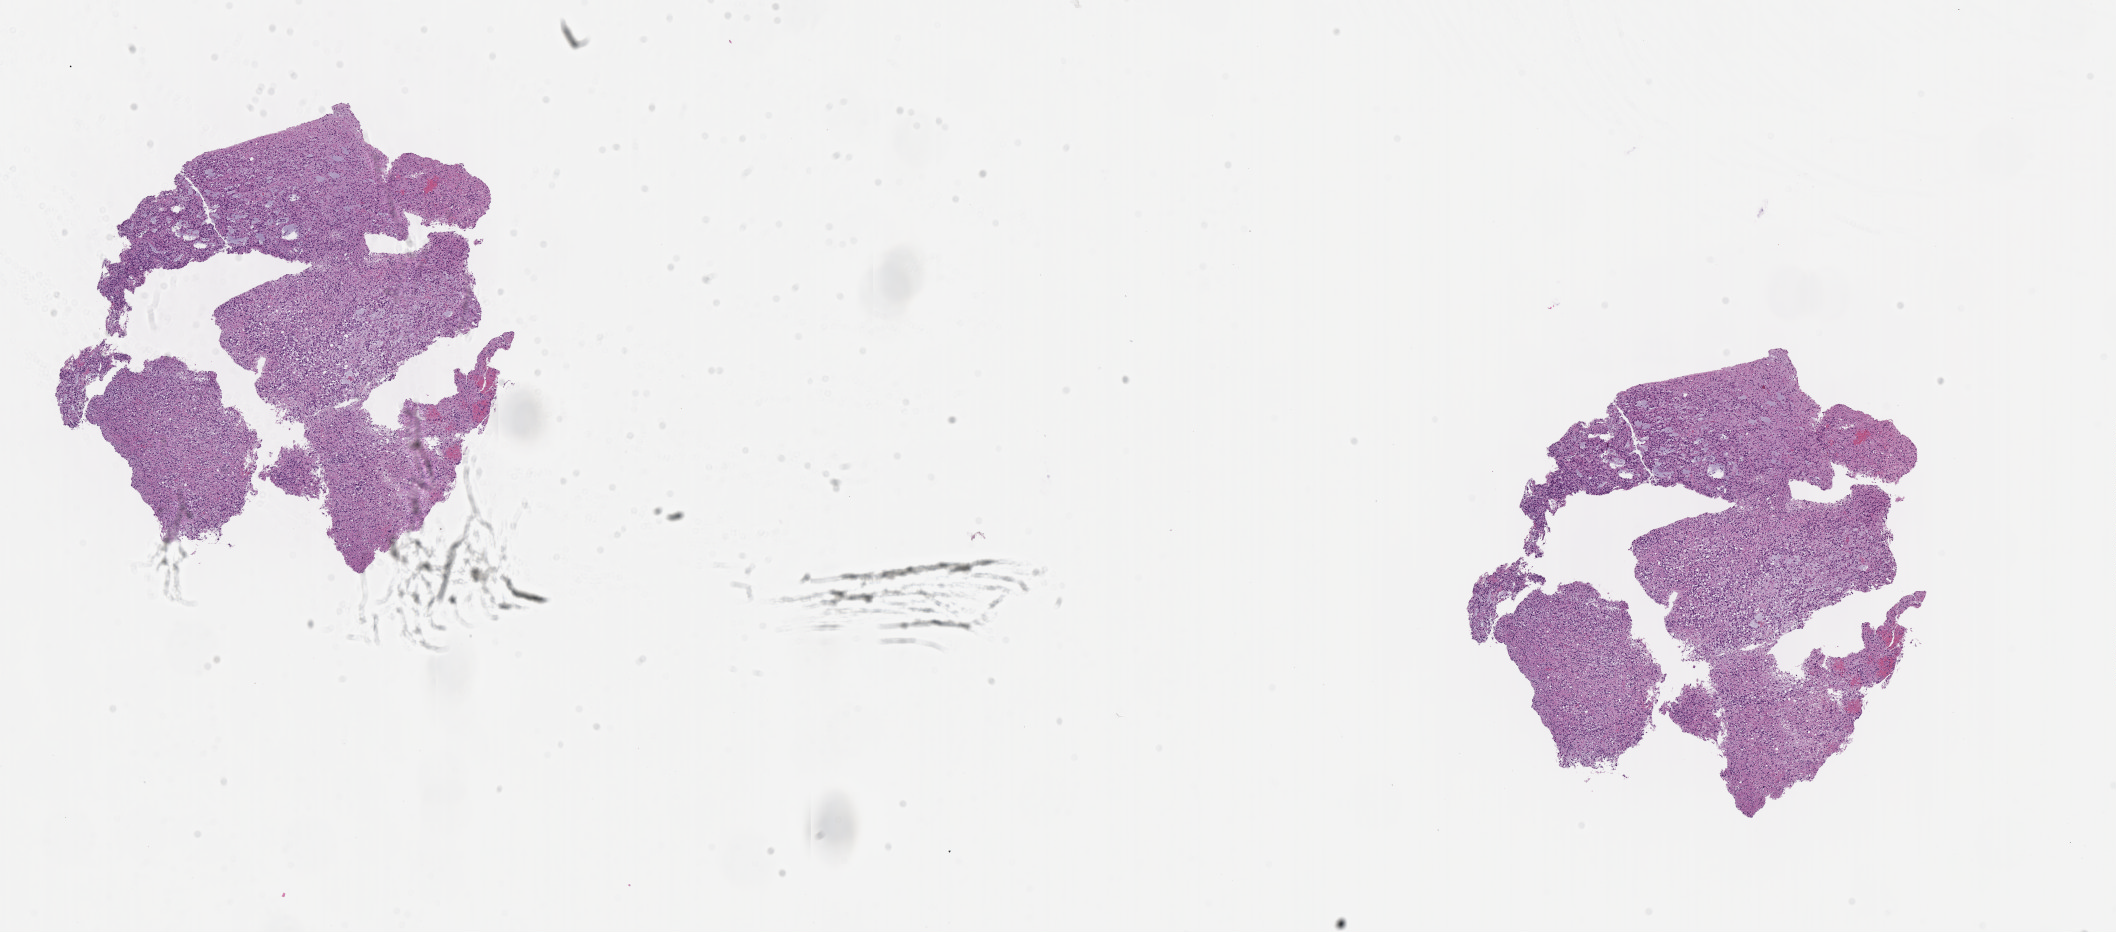
Digitized H&E tissue section (whole slide), a low-resolution overview of the entire scanned area, about 17.1 x 7.5 mm (slide scanned at 40x); formalin-fixed paraffin-embedded (FFPE) diagnostic section; primary tumour sample from the brain. Patient: female, age at initial diagnosis 27 years. Histologic grade: G3 (poorly differentiated).
Pathologic diagnosis: Astrocytoma, anaplastic (cerebrum).